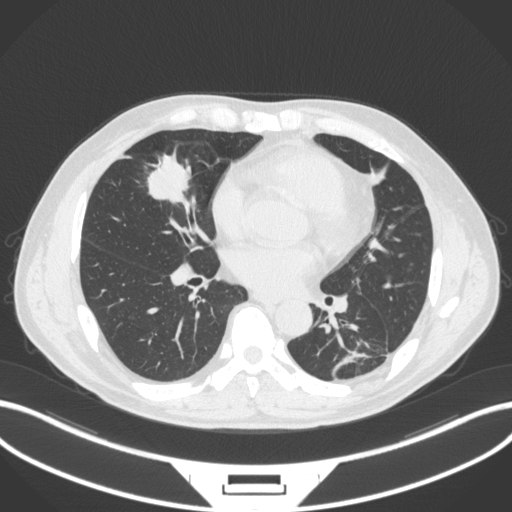
Chest CT, one axial slice. Position 134 of 399 along the scan axis. Reconstruction kernel B31f. Lung window (W 1500 / L -600 HU). 1 mm slice thickness. 512 × 512 image matrix, field of view 400 × 400 mm. Patient: male, 59 years. Case-level facts recorded for this patient, not image findings: clinical TNM (as recorded): T2a N1 M0.
Structures marked on this image (rectangle marked by the reading radiologist):
- lung tumour (recorded histology: adenocarcinoma): box from (x=143, y=150) to (x=196, y=204) px